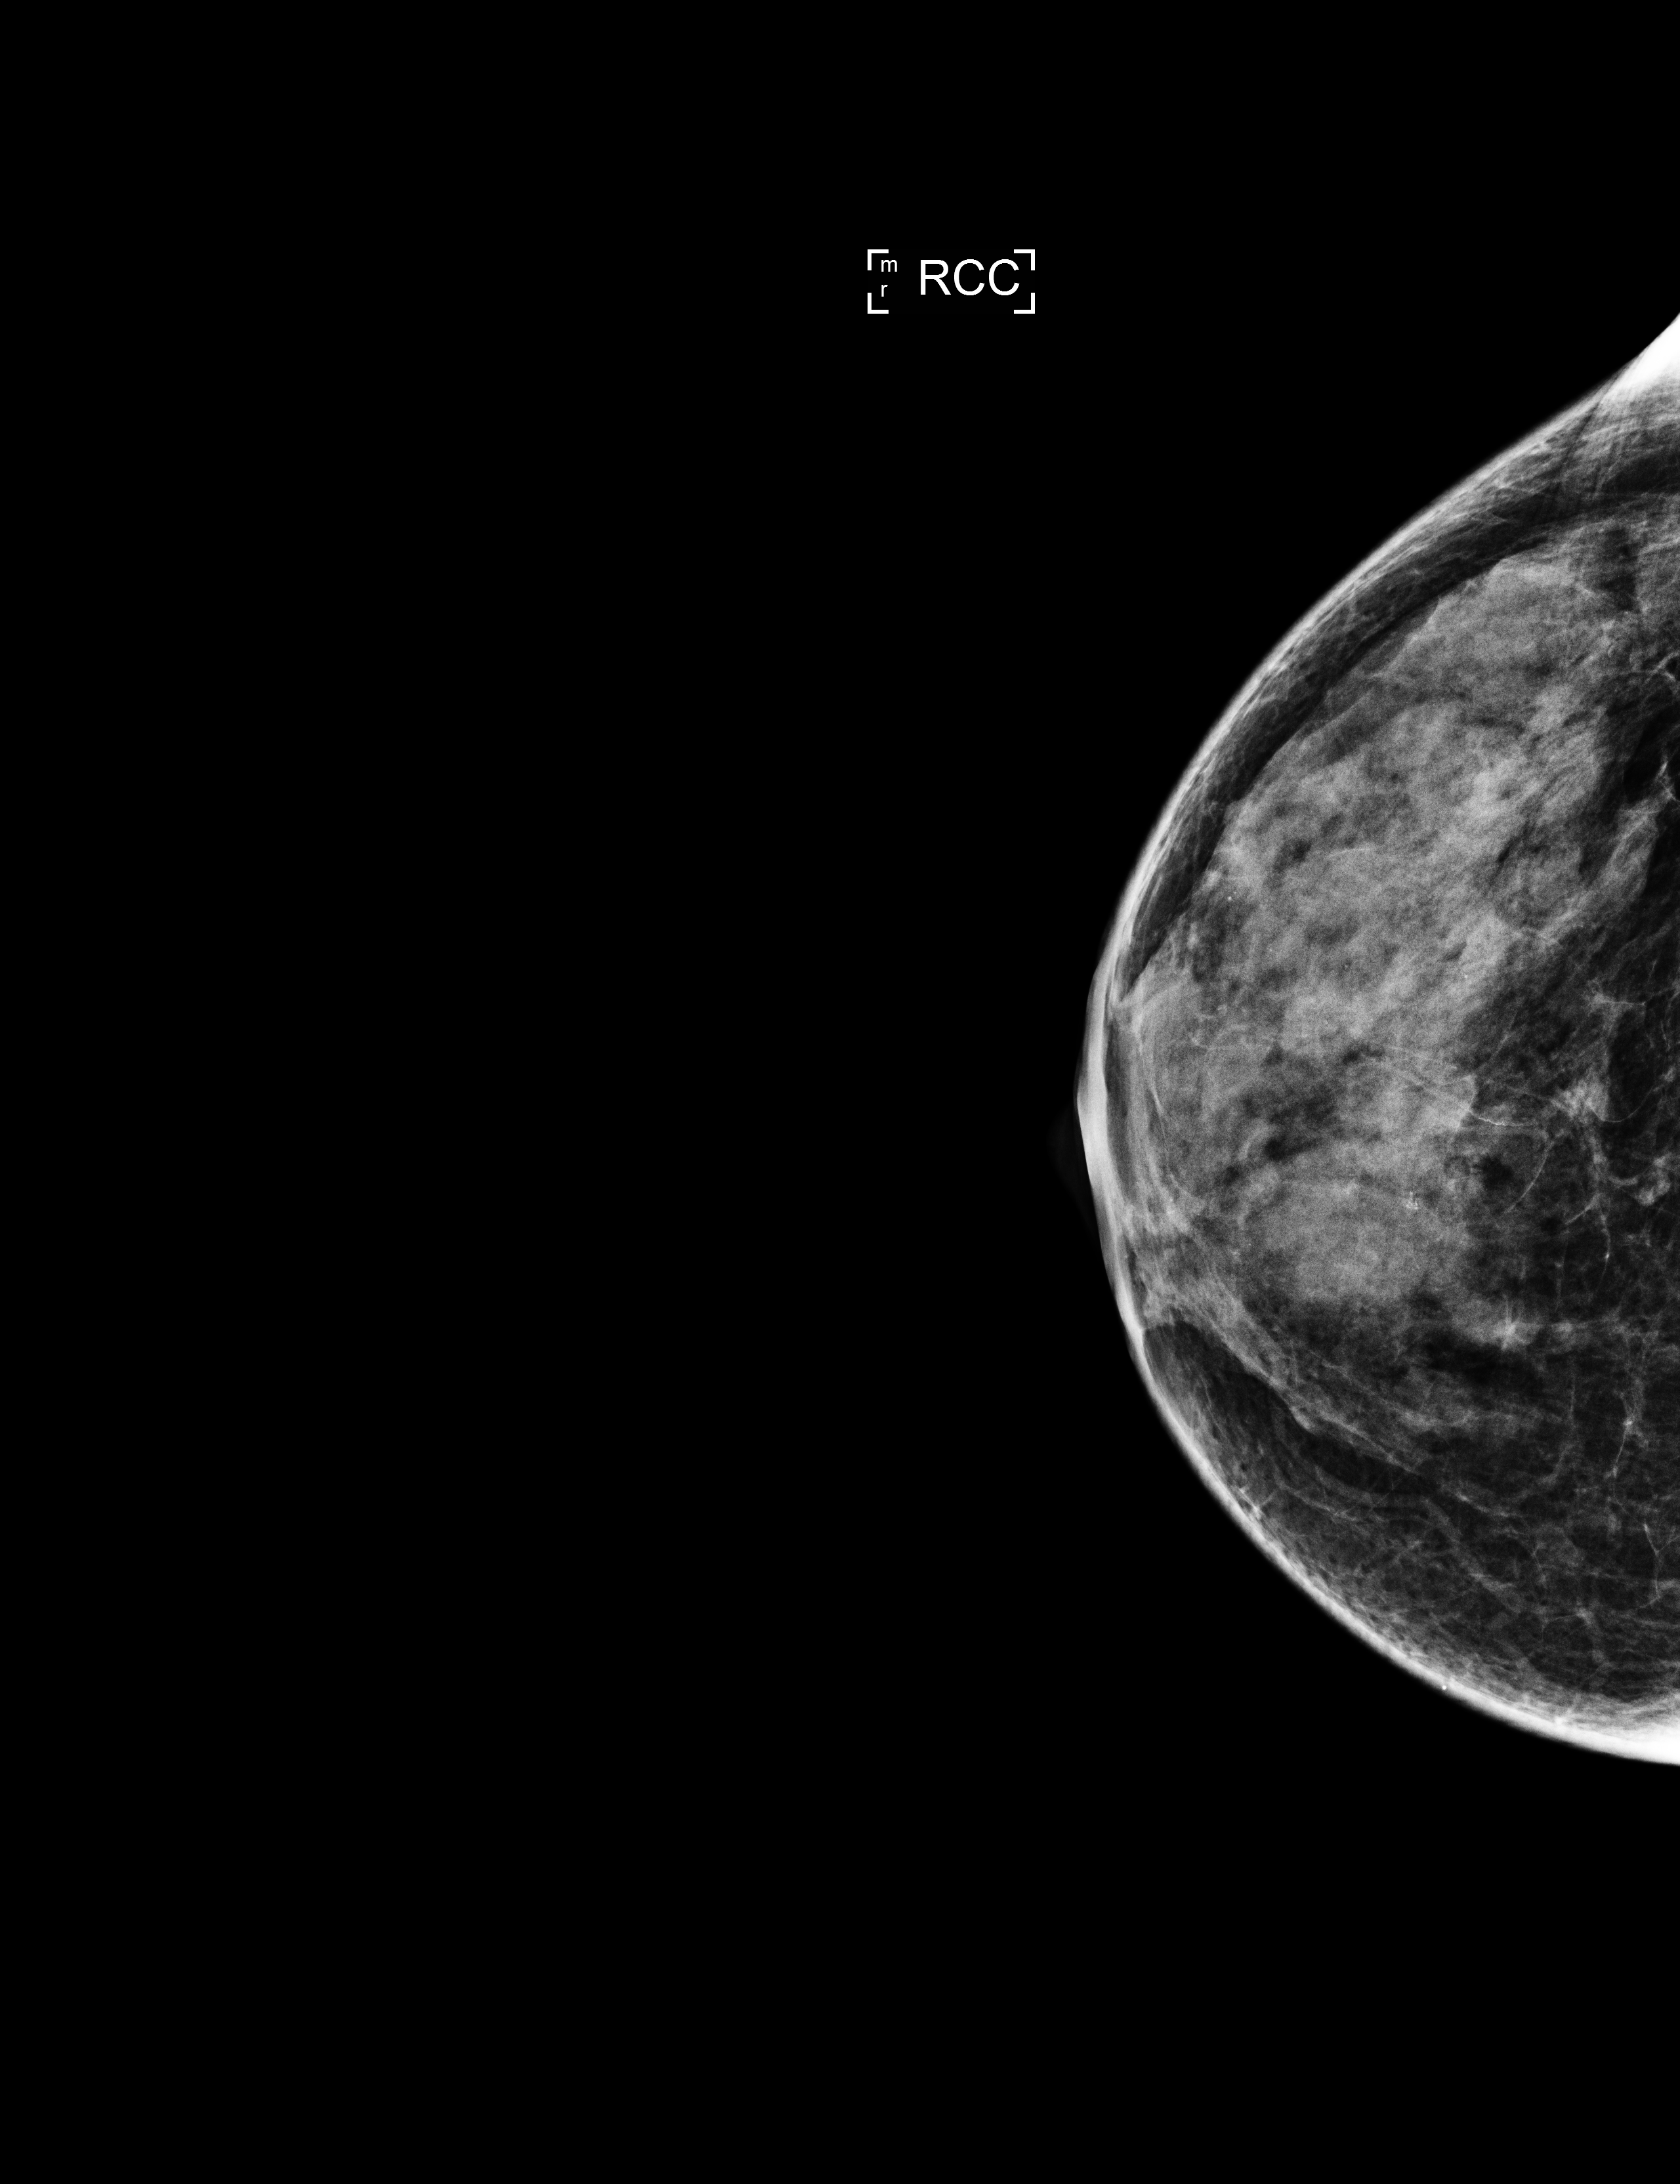
Full-field digital mammogram (FFDM); right breast; craniocaudal (CC) view; screening examination. Female patient, age 50 years.
Breast density at the screening exam (both breasts): extremely dense (BI-RADS density category d). Final BI-RADS assessment for this screening round (tomosynthesis exam, both breasts): category 3. Recall: recalled for additional imaging after this screen.